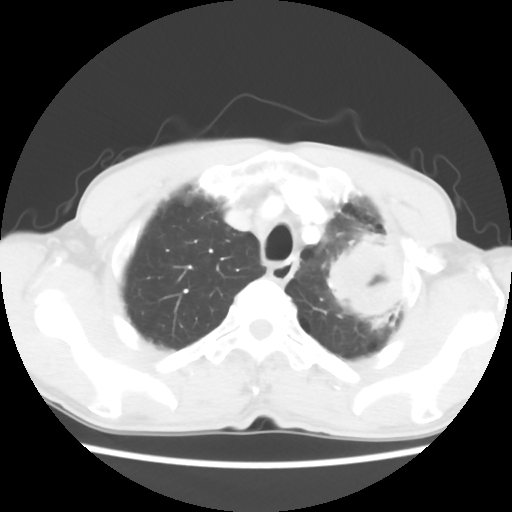
Chest CT, one axial slice. Slice 50 of 60 in the series (ordered by position). Reconstruction kernel STANDARD. Lung window (W 1500 / L -600 HU). 5 mm slice thickness. 512 × 512 image matrix. Patient: male, 64 years. Case-level facts recorded for this patient, not image findings: clinical TNM (as recorded): T3 N3 M0.
Annotated regions visible in this slice (bounding box drawn by a radiologist):
- lung tumour (recorded histology: adenocarcinoma): bounding box (x1, y1, x2, y2) in pixels: (319, 224, 405, 332)